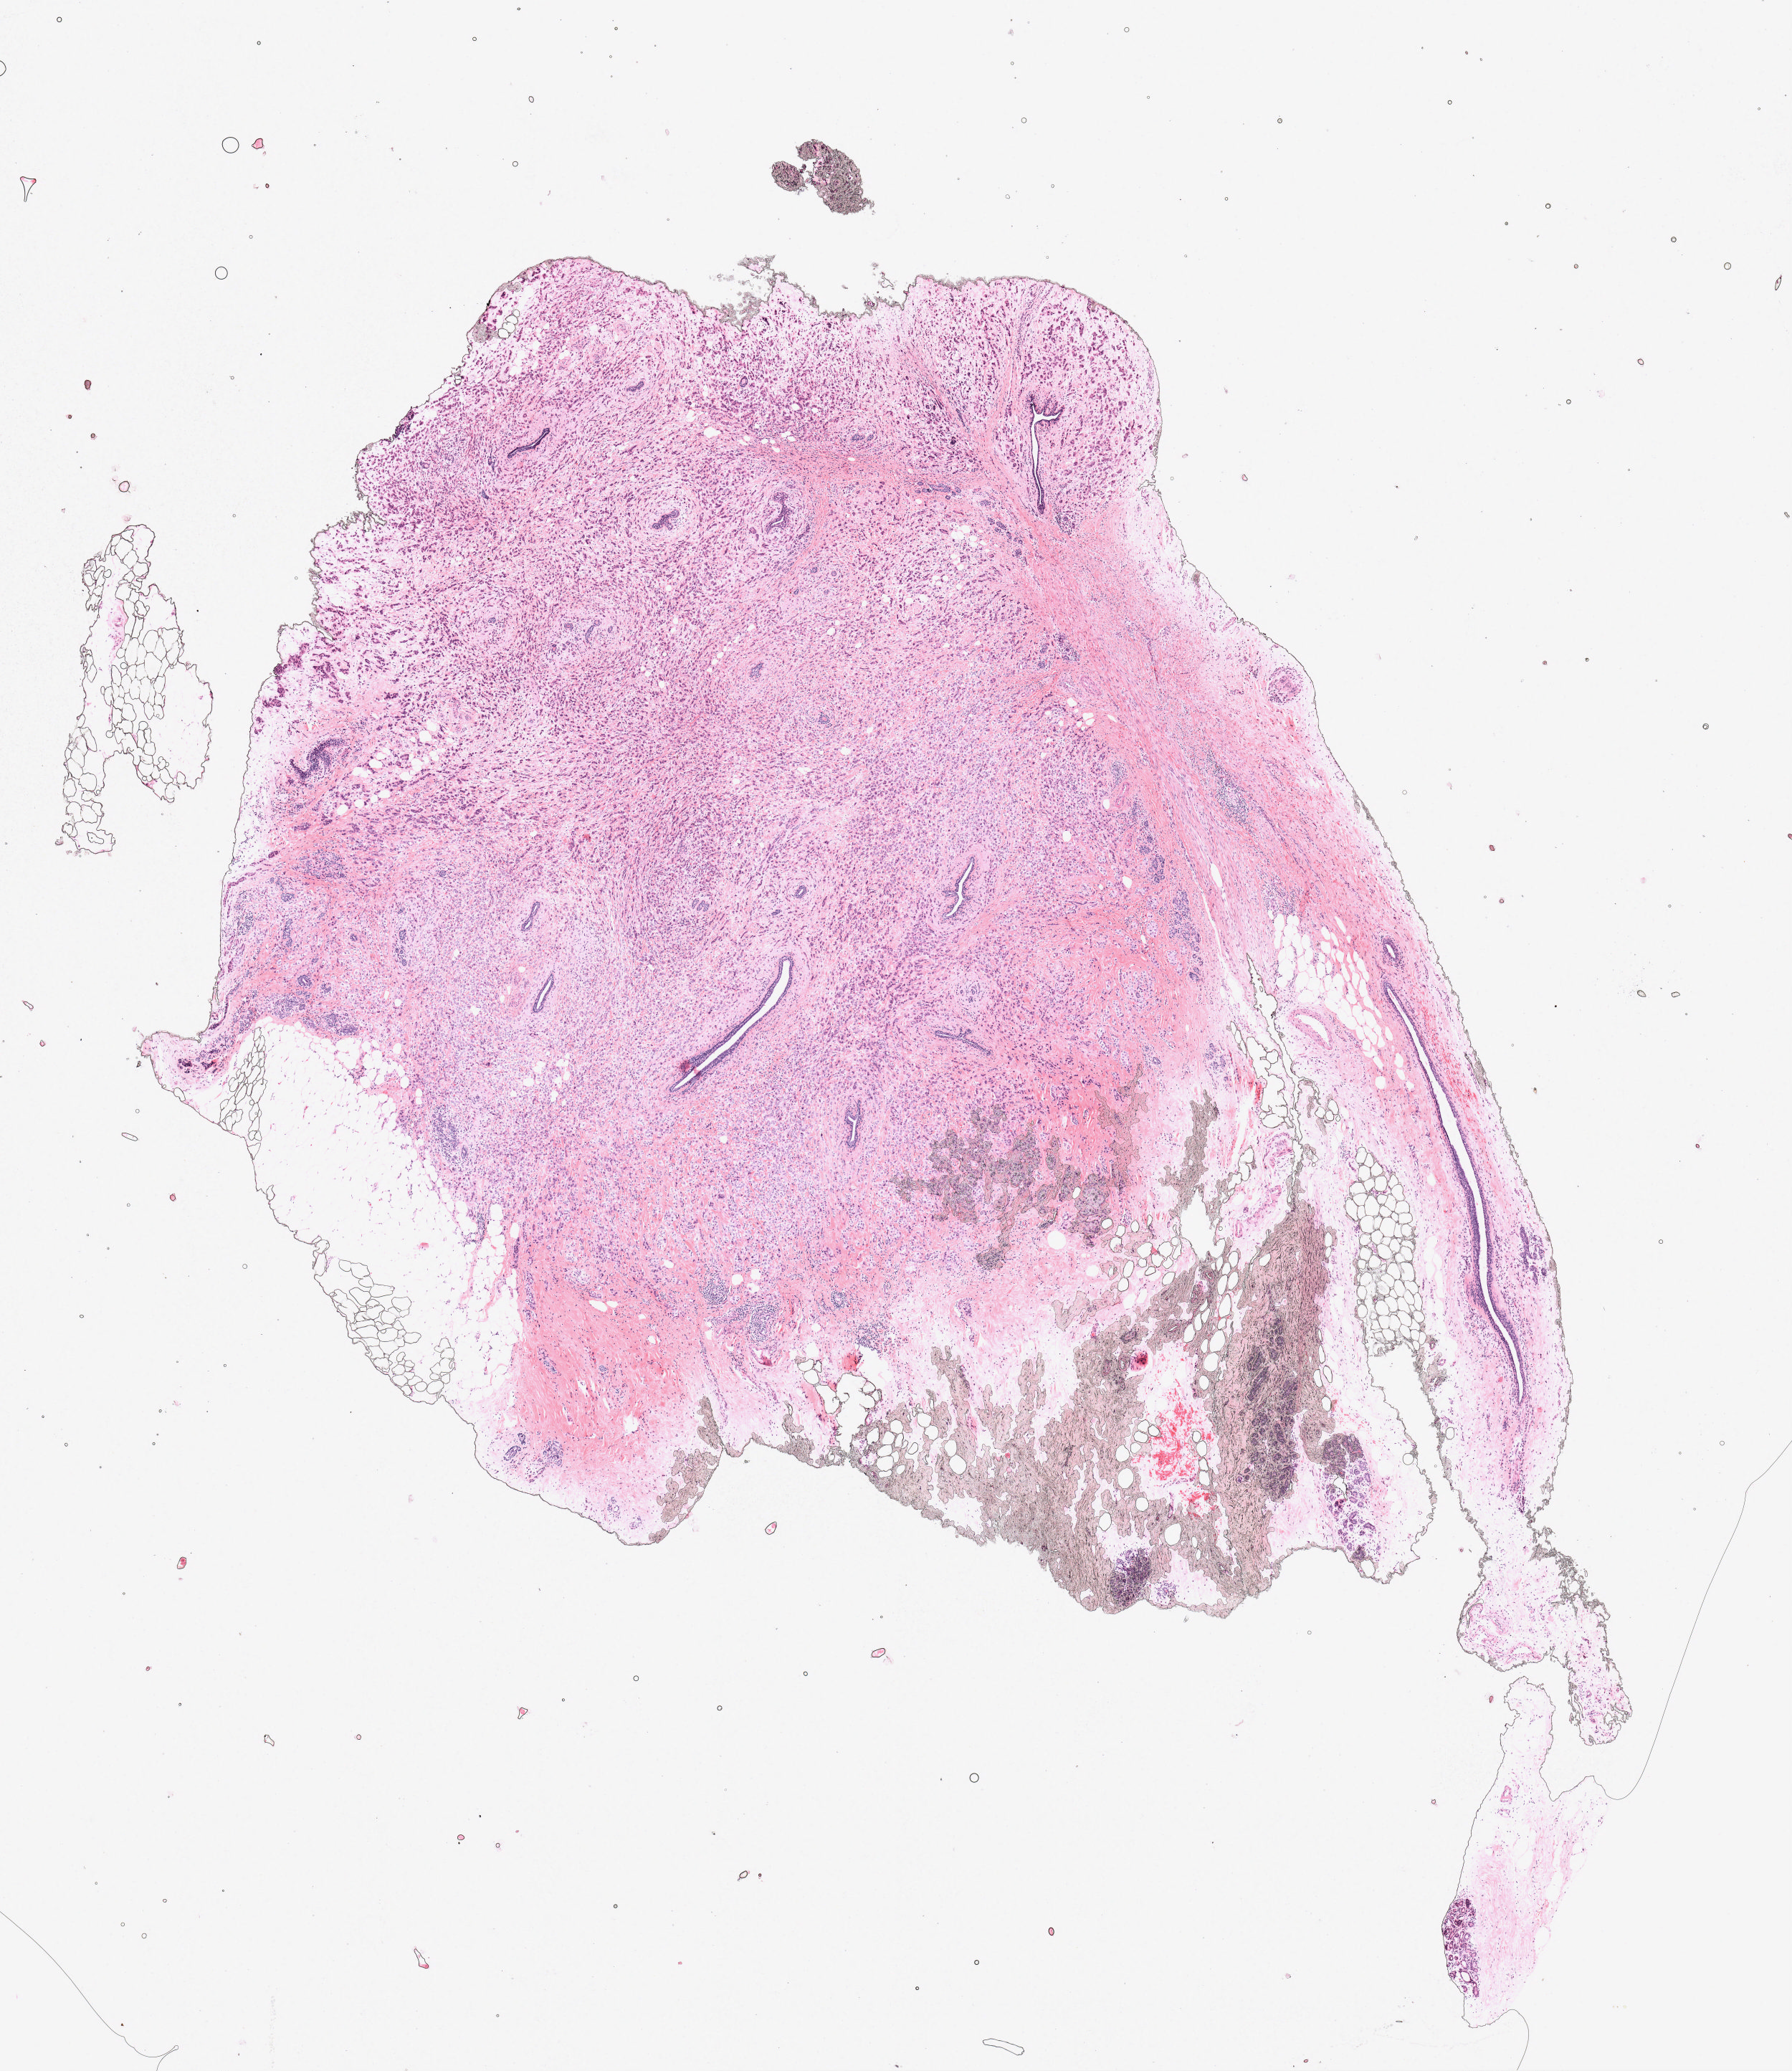
Digitized Hematoxylin and eosin (H&E) stained tissue section (whole slide), low-resolution overview of the scanned area, about 10.0 x 11.5 mm (acquisition: 20x scan), formalin-fixed paraffin-embedded (FFPE) diagnostic section, primary tumour sample from the breast. Female patient; age at initial diagnosis 44 years.
• histologic diagnosis: Lobular carcinoma, NOS
• lymph nodes positive (case pathology): 2 of 18 examined
• AJCC pathologic stage: IIB (7th edition)